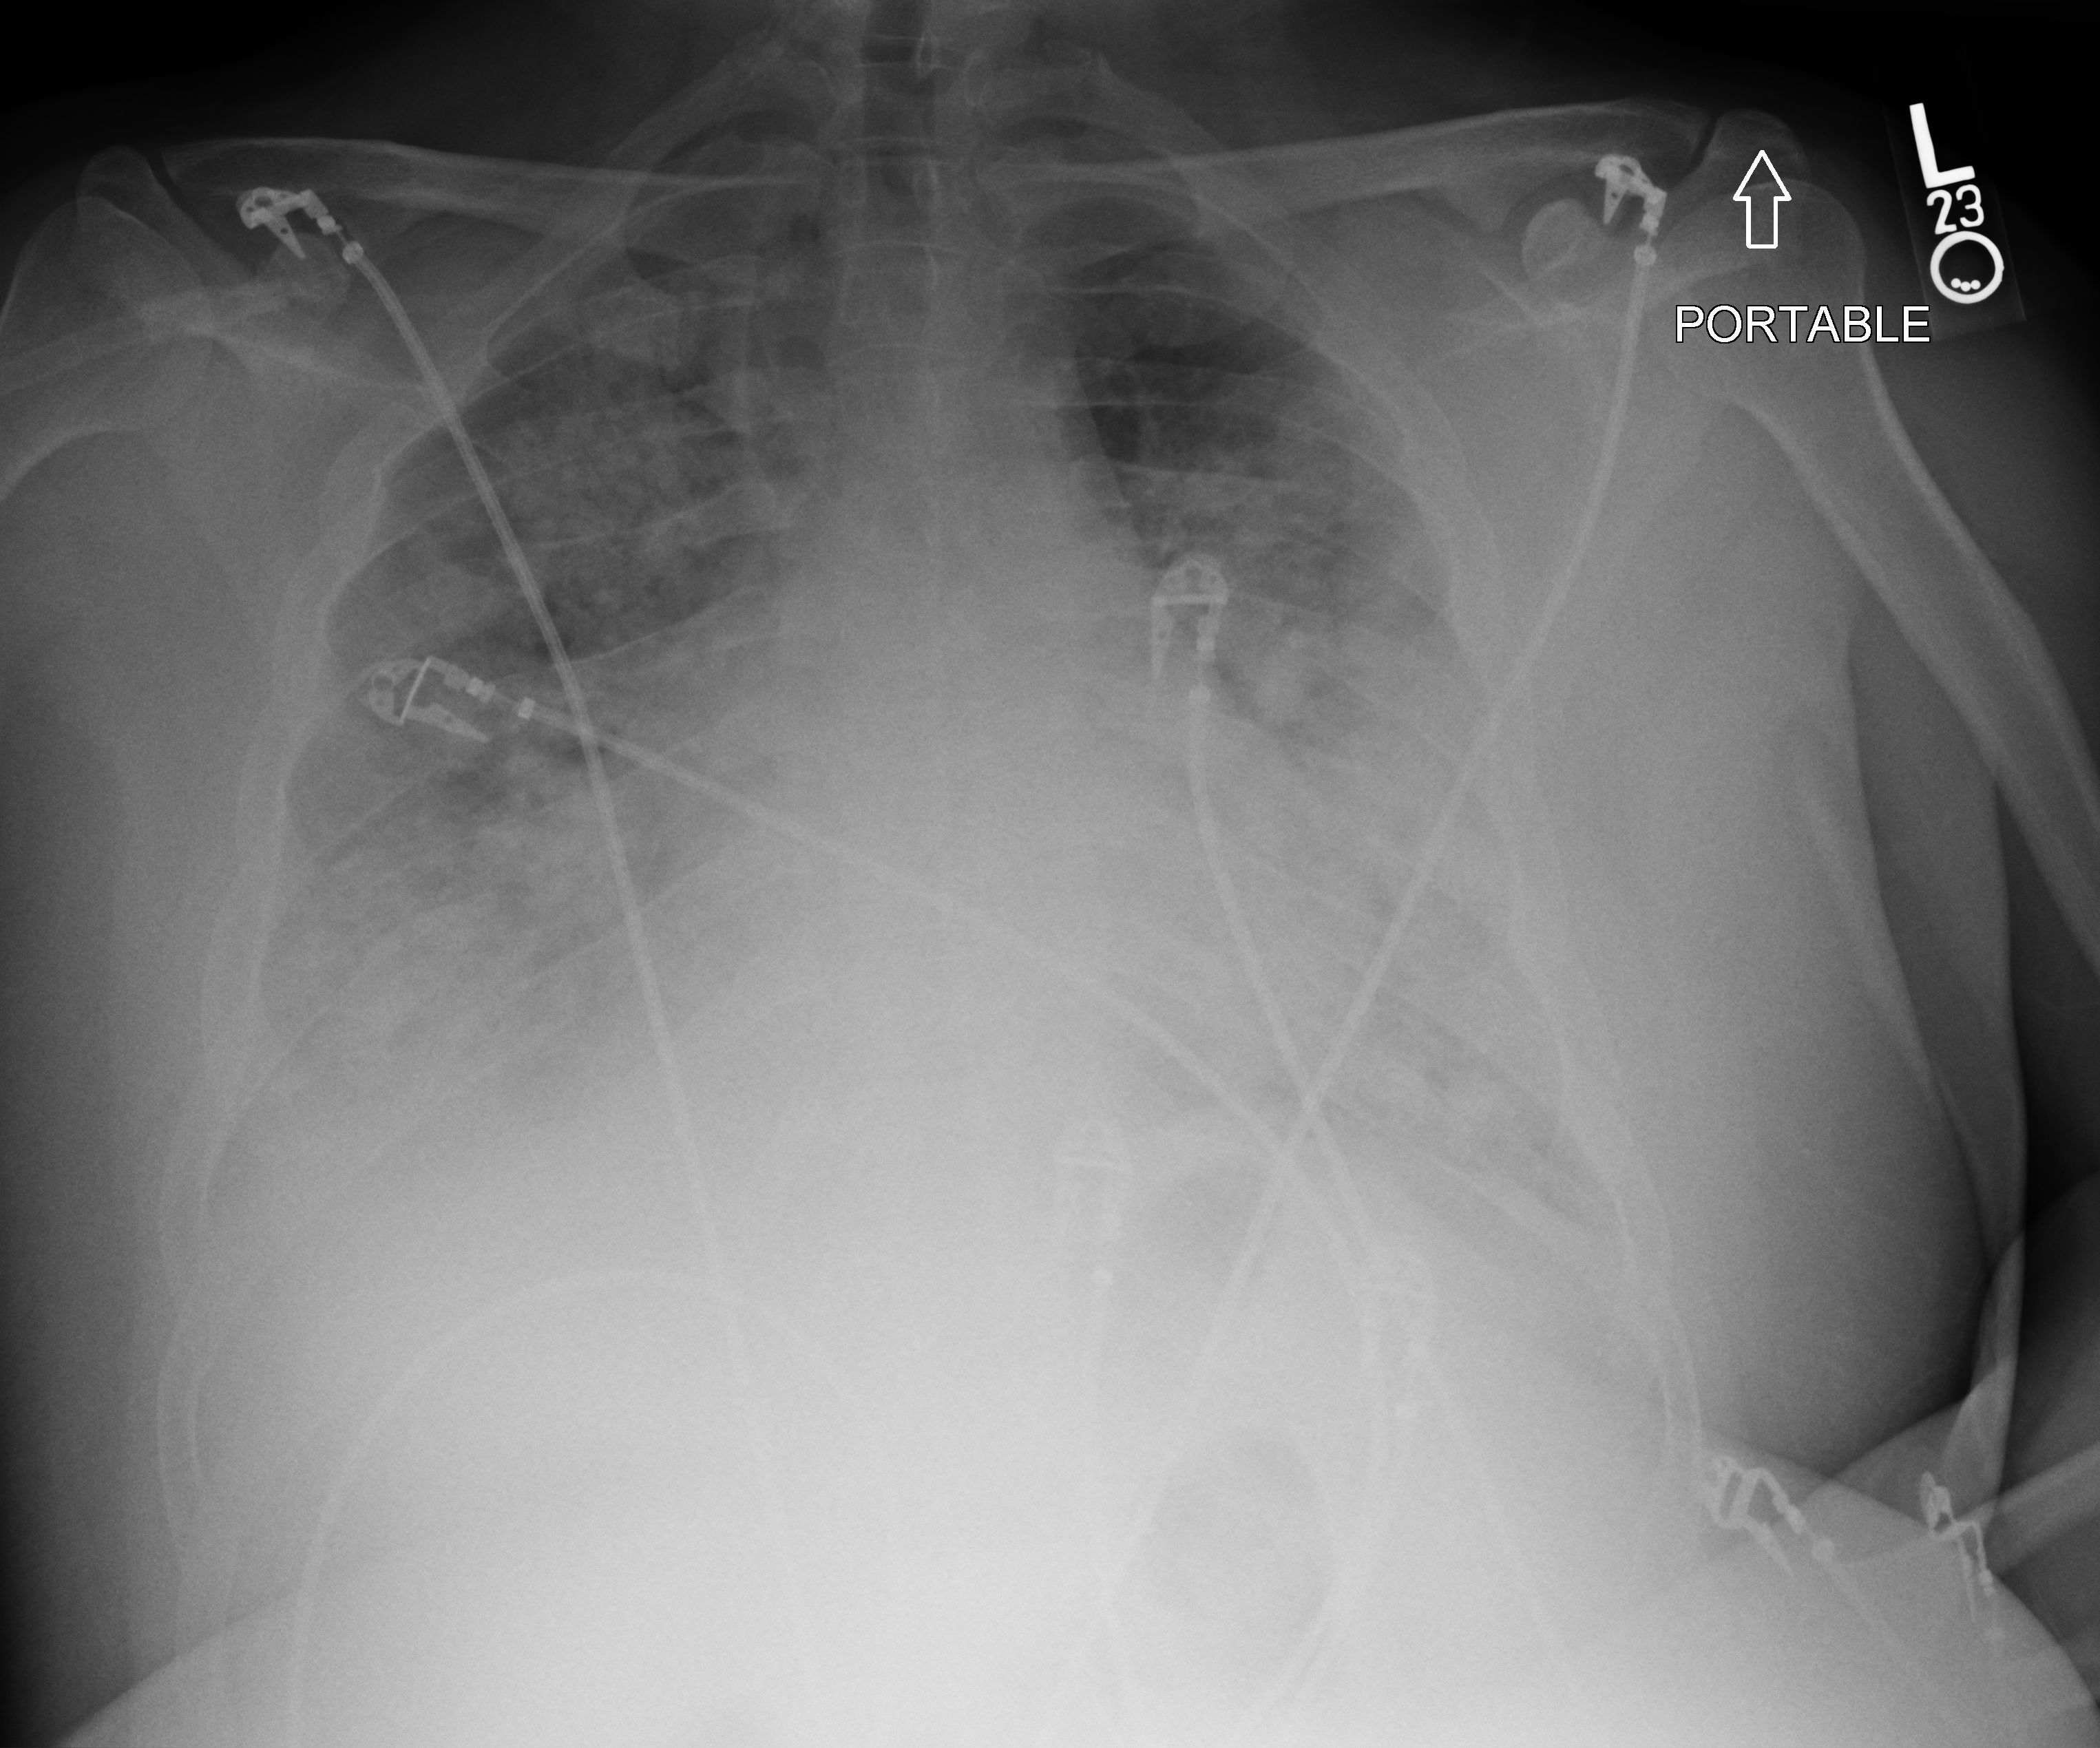
Chest X-ray (portable), anteroposterior (AP) projection. Patient hospitalised with COVID-19, aged 18–59 years.
From the hospital-stay record, not from the radiograph (when in the stay this image was taken is not recorded):
- mechanically ventilated during this hospital stay: yes